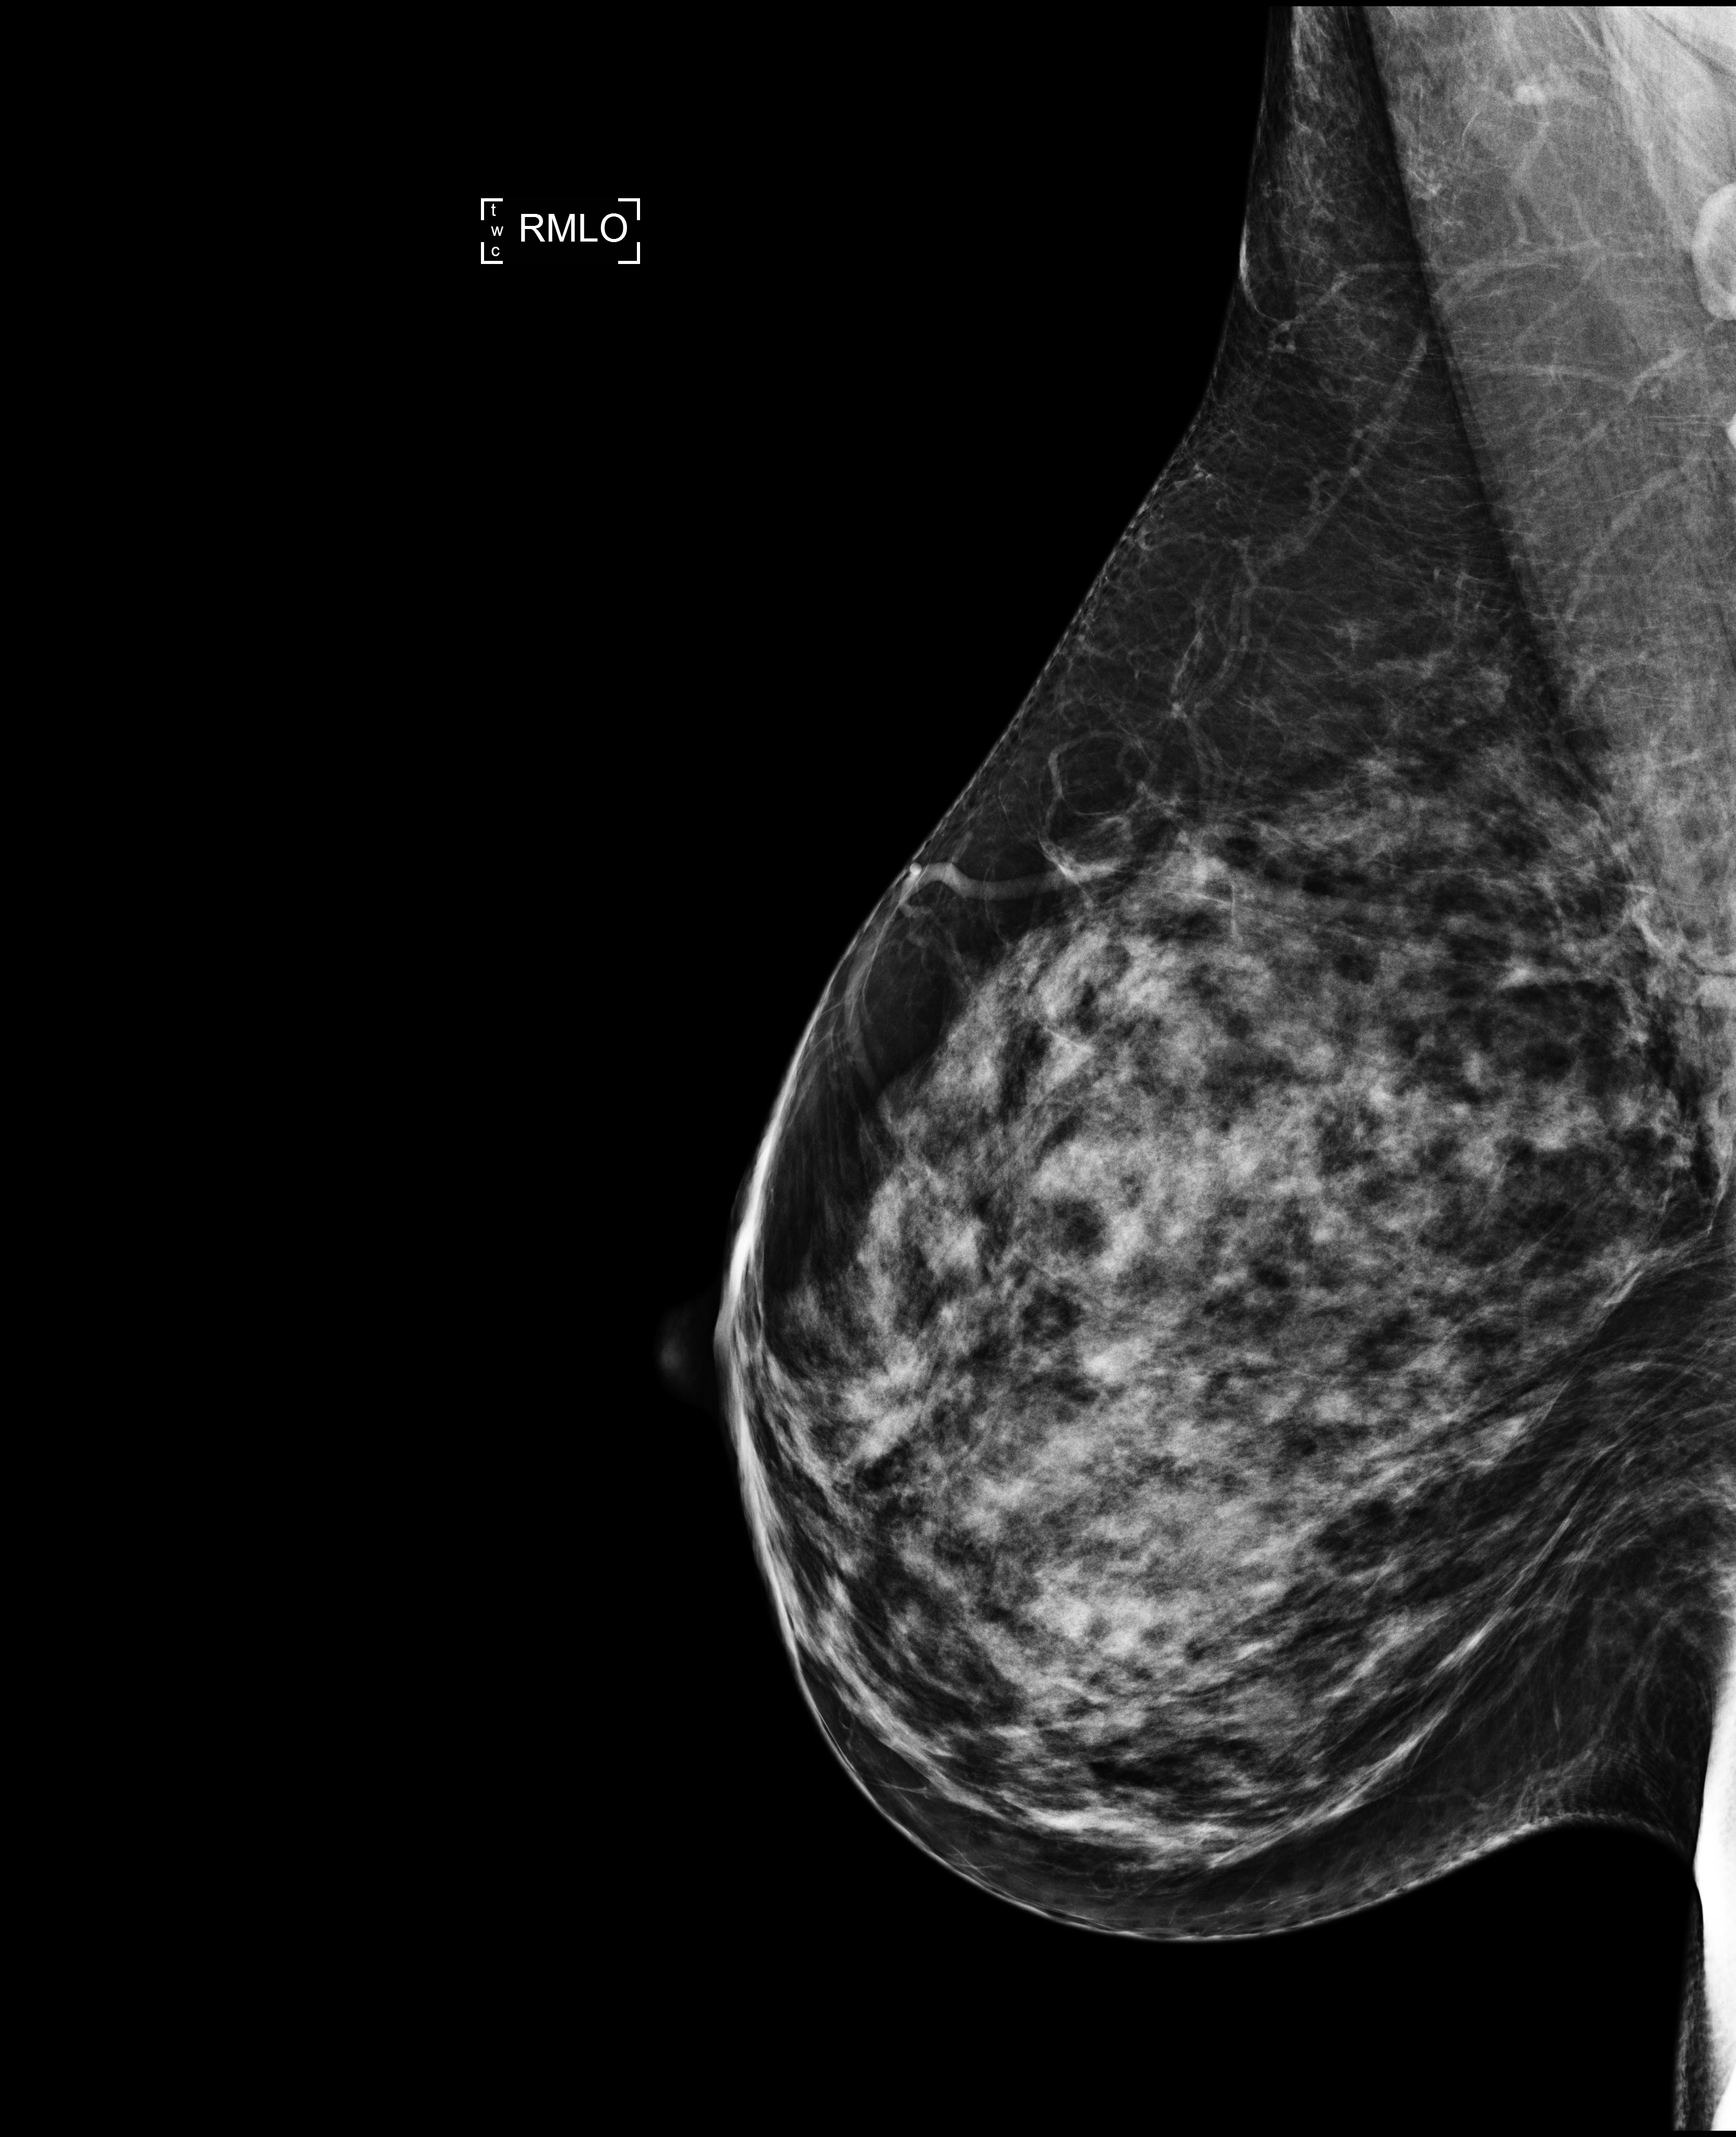
Full-field digital mammogram (FFDM); right breast; mediolateral oblique (MLO) view; annual screening mammography examination; compressed breast thickness 69 mm; system: Selenia Dimensions. Patient: female, 44 years.
Breast density at the screening exam (both breasts): heterogeneously dense (BI-RADS density category c). Final BI-RADS assessment for this screening round (tomosynthesis exam, both breasts): category 2. Recall: no recall after this screen.